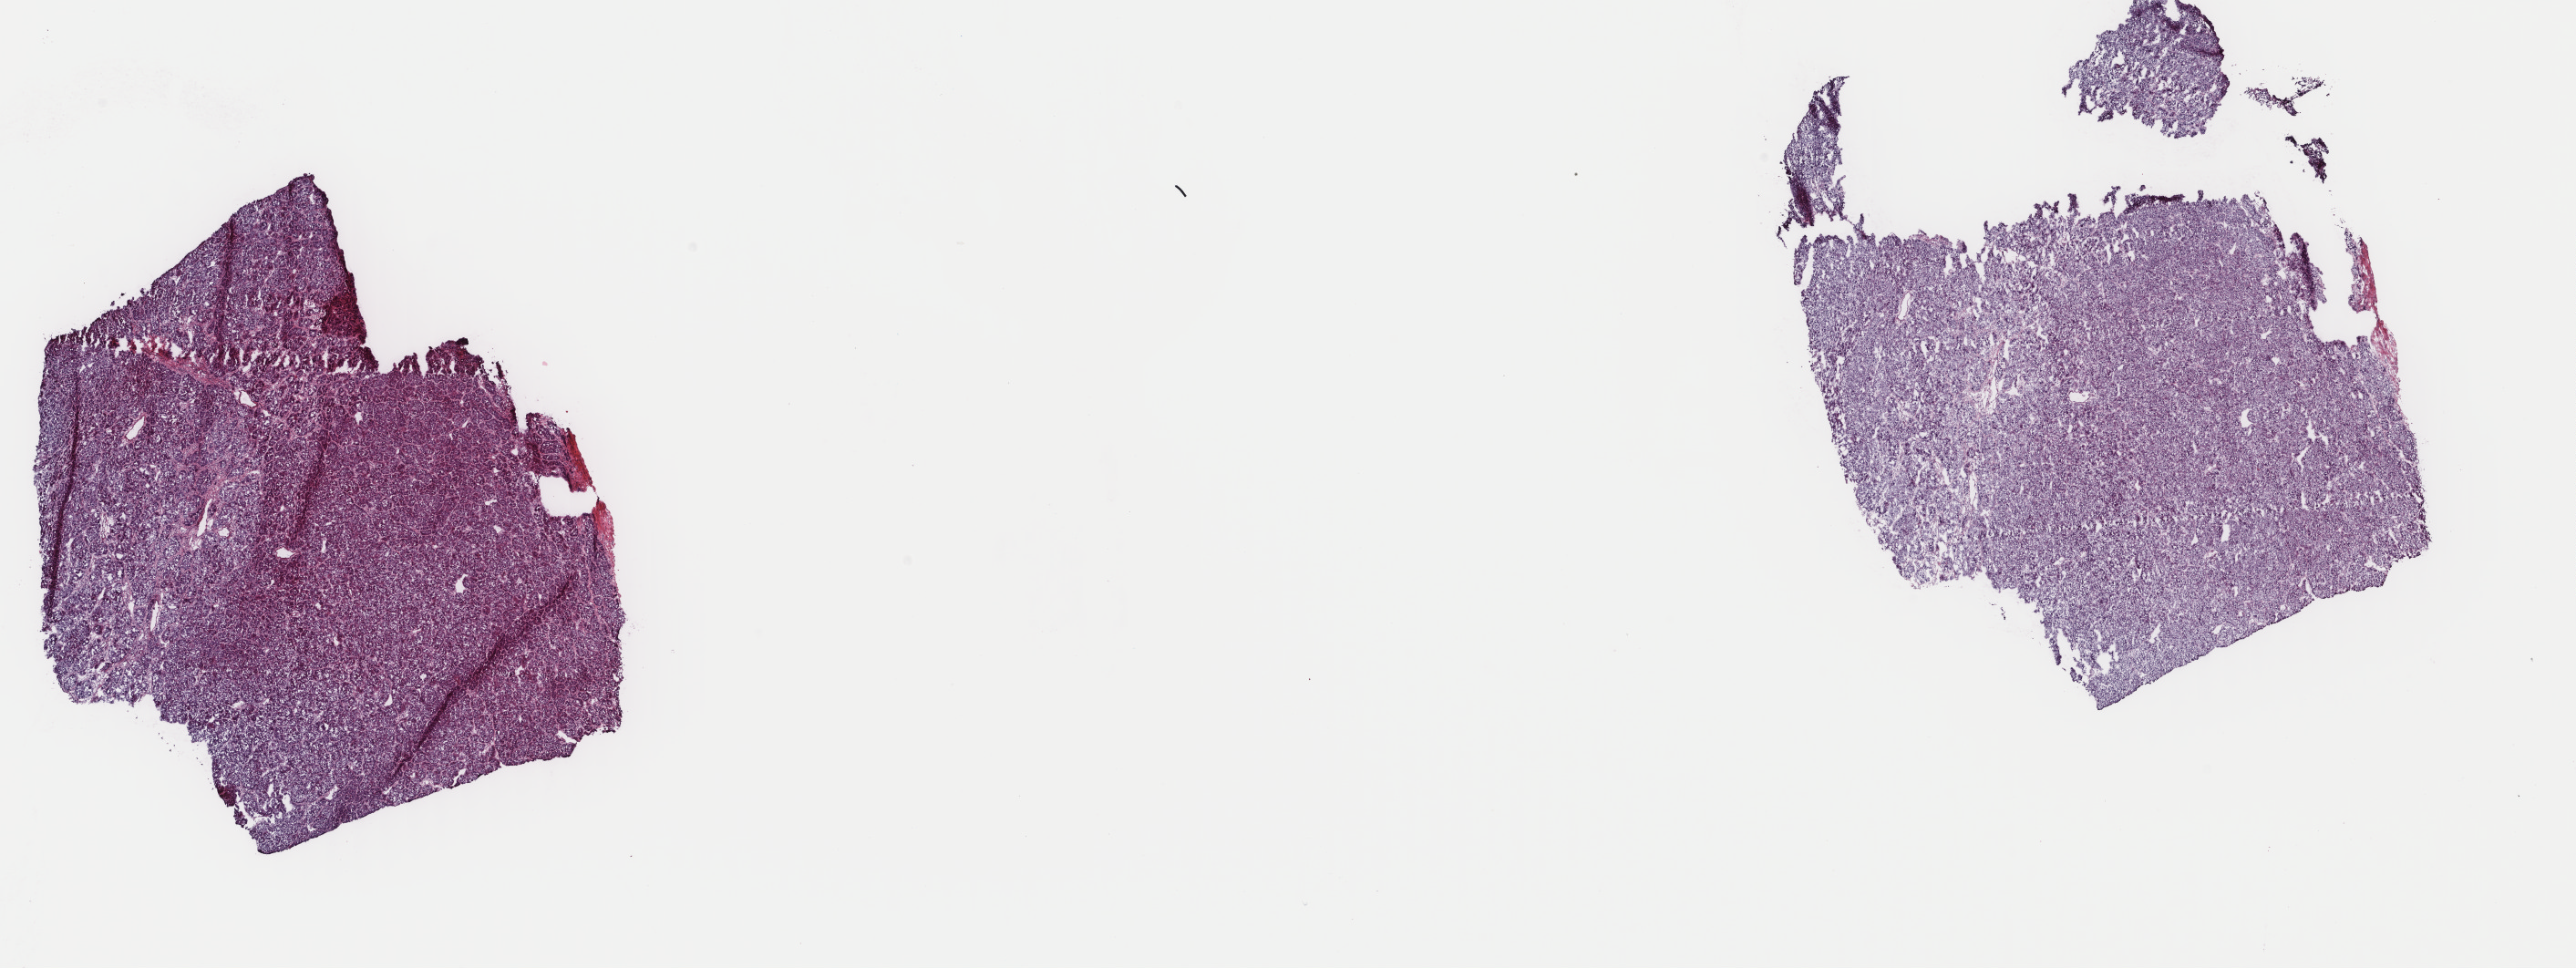
Digitized H&E-stained tissue section (whole slide) — whole scanned area (about 22.4 x 8.4 mm, from a 40x scan) shown as a low-resolution overview. Frozen section from the top of the tissue portion. Liver, primary tumour sample. Male patient; age at initial diagnosis 68 years. Histologic grade: G2 (moderately differentiated). Pathologist review of this section (percent, as recorded): tumour cells 100%, tumour nuclei 80%, normal cells 0%, stromal cells 0%, necrosis 0%. Inflammatory infiltration, as recorded: lymphocyte infiltration 3%, monocyte infiltration 0%, neutrophil infiltration 0%.
Histologic diagnosis: Hepatocellular carcinoma, NOS.